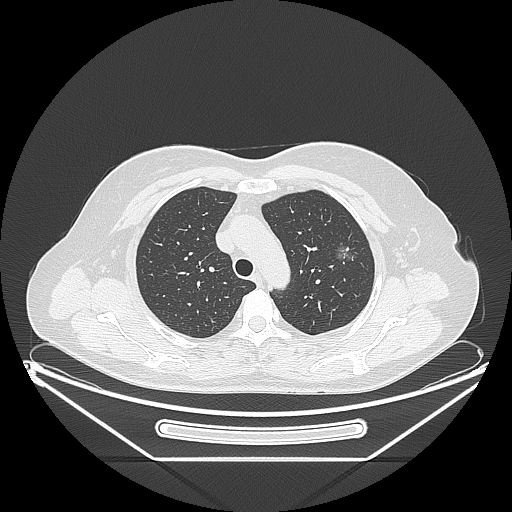
Chest CT, one axial slice; position 166 of 226 along the scan axis; lung window (W 1500 / L -600 HU); 1.25 mm slice thickness; 512 × 512 image matrix, field of view 447 × 447 mm. Female patient, age 54 years. From the clinical record (not read from this slice): clinical TNM (as recorded): T1c N0 M0.
Outlined on this slice (rectangle marked by the reading radiologist):
- lung tumour (recorded histology: adenocarcinoma): bounding box (x1, y1, x2, y2) in pixels: (333, 239, 361, 274)